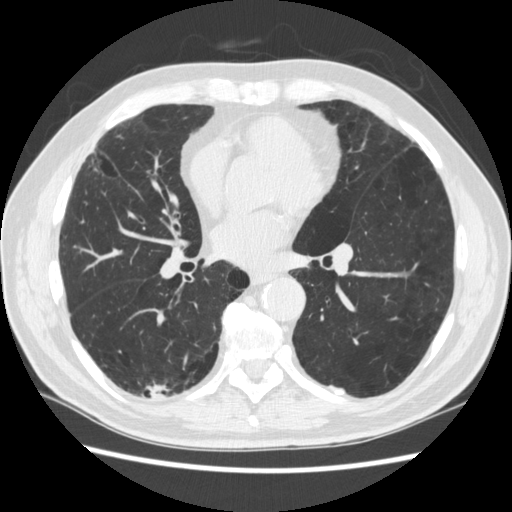
Low-dose screening chest CT, one axial slice; position 127 of 266 along the scan axis; 120 kVp; lung window (W 1500 / L -600 HU); 512 × 512 image matrix.
Structures marked on this image (outlined manually by an expert reader):
- lesion 1 (tumor, upper lobe of right lung): bounding box (x1, y1, x2, y2) in pixels: (150, 385, 164, 399)